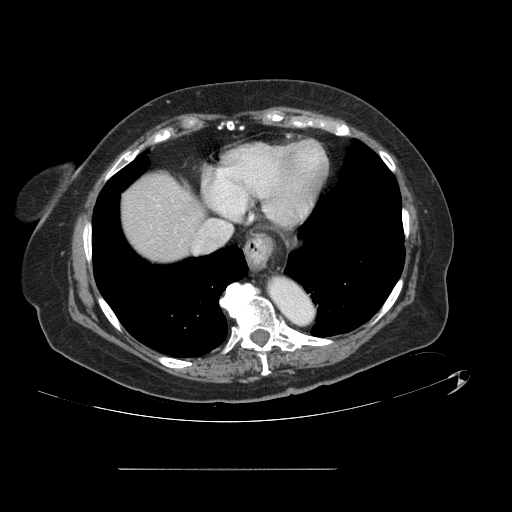
Contrast-enhanced abdominal CT, one axial slice; position 123 of 148 along the scan axis; 120 kVp; intravenous contrast given; soft-tissue window (W 400 / L 40 HU); 512 × 512 image matrix, field of view 439 × 439 mm. Female patient, age 75 years. From the clinical record (not read from this slice): diagnosis: colorectal cancer liver metastases, imaged before liver resection; multiple liver metastases: no; largest metastasis: 2.4 cm; disease in both lobes: no.
Structures marked on this image (manually delineated by an expert):
- hepatic veins: bounding box (x1, y1, x2, y2) in pixels: (218, 222, 229, 228)
- liver: (123, 174, 203, 262)
- planned liver remnant (the part of the liver to remain after resection): (123, 174, 203, 262)